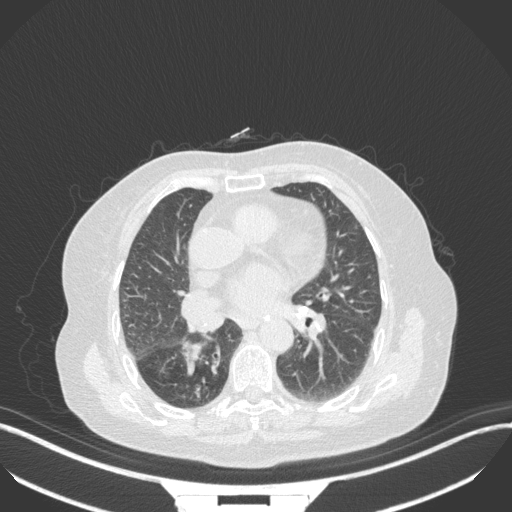
Chest CT, one axial slice; slice 154 of 329 in the series (ordered by position); reconstruction kernel B31f; lung window (W 1500 / L -600 HU); 1 mm slice thickness; 512 × 512 image matrix. Patient: female, 75 years. Case-level facts recorded for this patient, not image findings: clinical TNM (as recorded): T1b N0 M1a; histopathological grade: G1.
Annotated regions visible in this slice (bounding box drawn by a radiologist):
- lung tumour (recorded histology: squamous cell carcinoma): bounding box <183,338,204,378> (left, top, right, bottom; pixels)